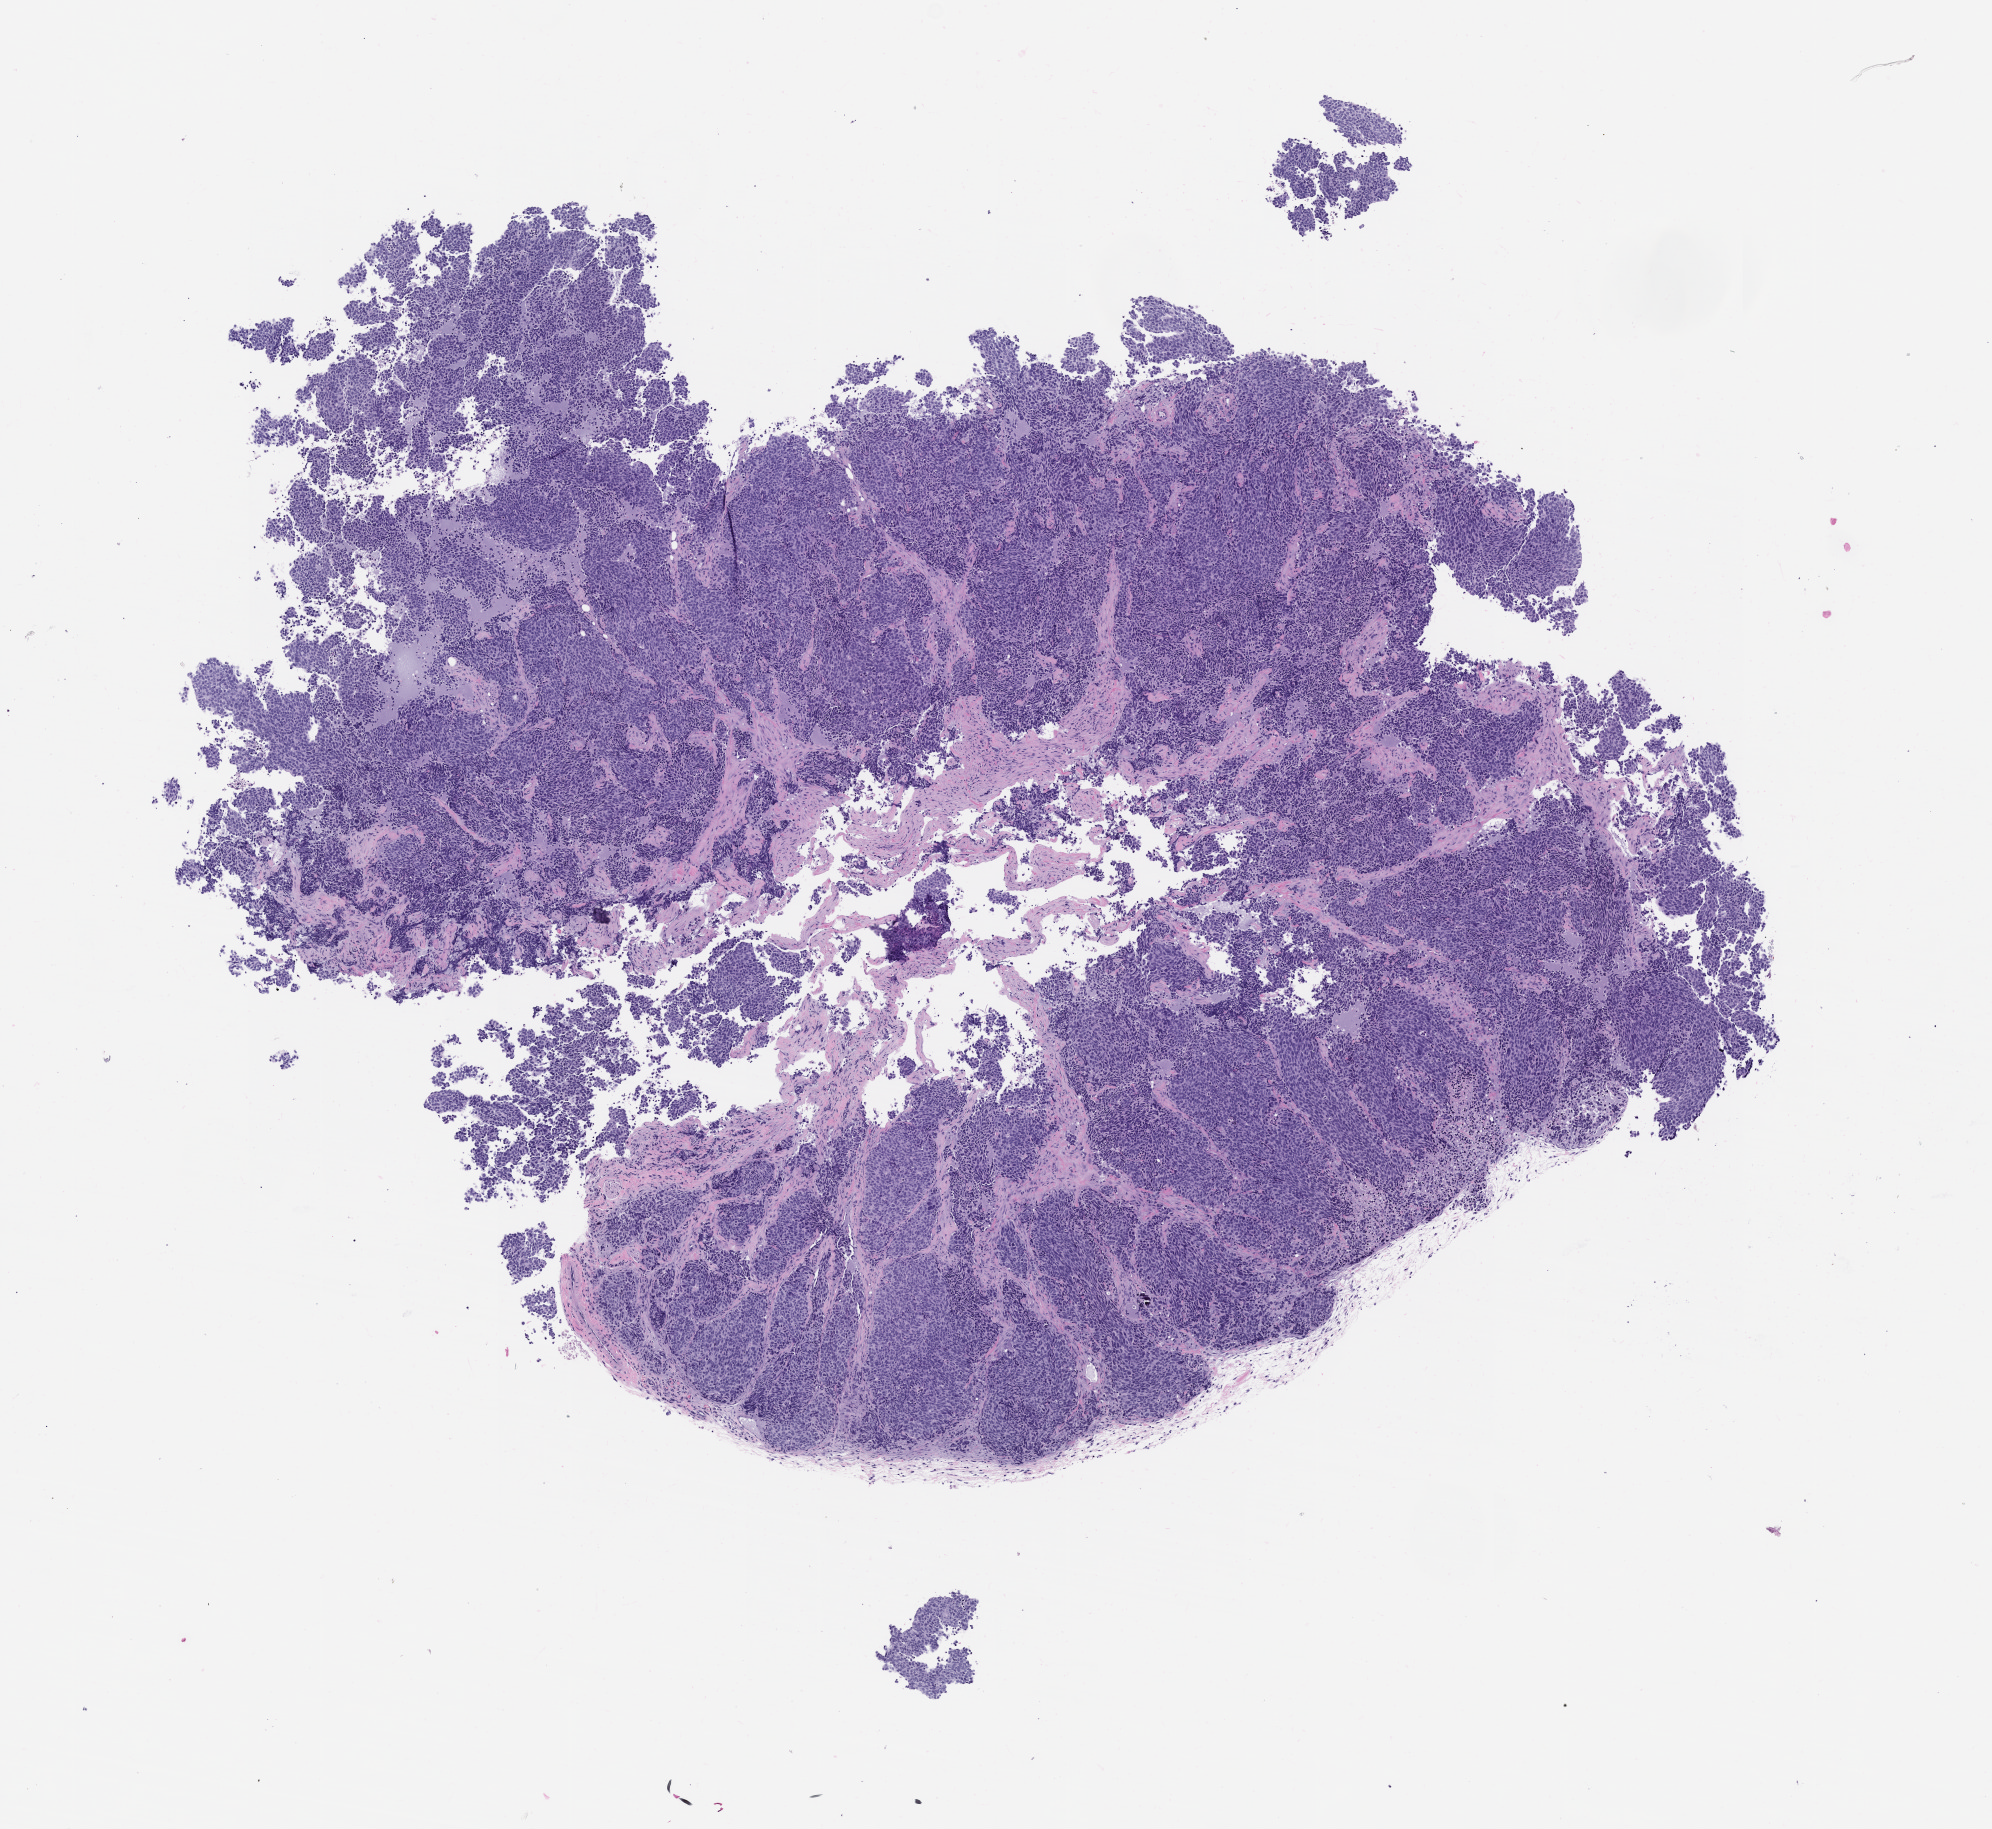
Whole-slide image, haematoxylin and eosin: patient-derived xenograft (human tumor grown in a mouse), whole scanned area (about 8.0 x 7.4 mm) shown as a low-resolution overview, formalin-fixed, paraffin-embedded (FFPE) tissue, originating tumor site category: lung.
• originating patient diagnosis: Lung Adenocarcinoma